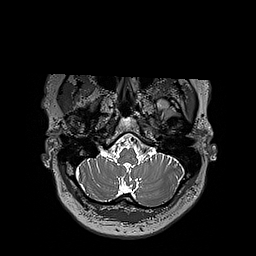
Brain MRI from a brain-tumour surgery series, one axial slice. Position 160 of 192 along the scan axis. 1 mm slice thickness. 256 × 256 image matrix, field of view 250 × 250 mm. Case-level facts recorded for this patient, not image findings: histopathology: Oligodendroglioma; WHO grade: 3; IDH mutation: yes.
Outlined on this slice (manually delineated by an expert):
- tumour: bounding box [x1, y1, x2, y2] px = [124, 97, 197, 107]